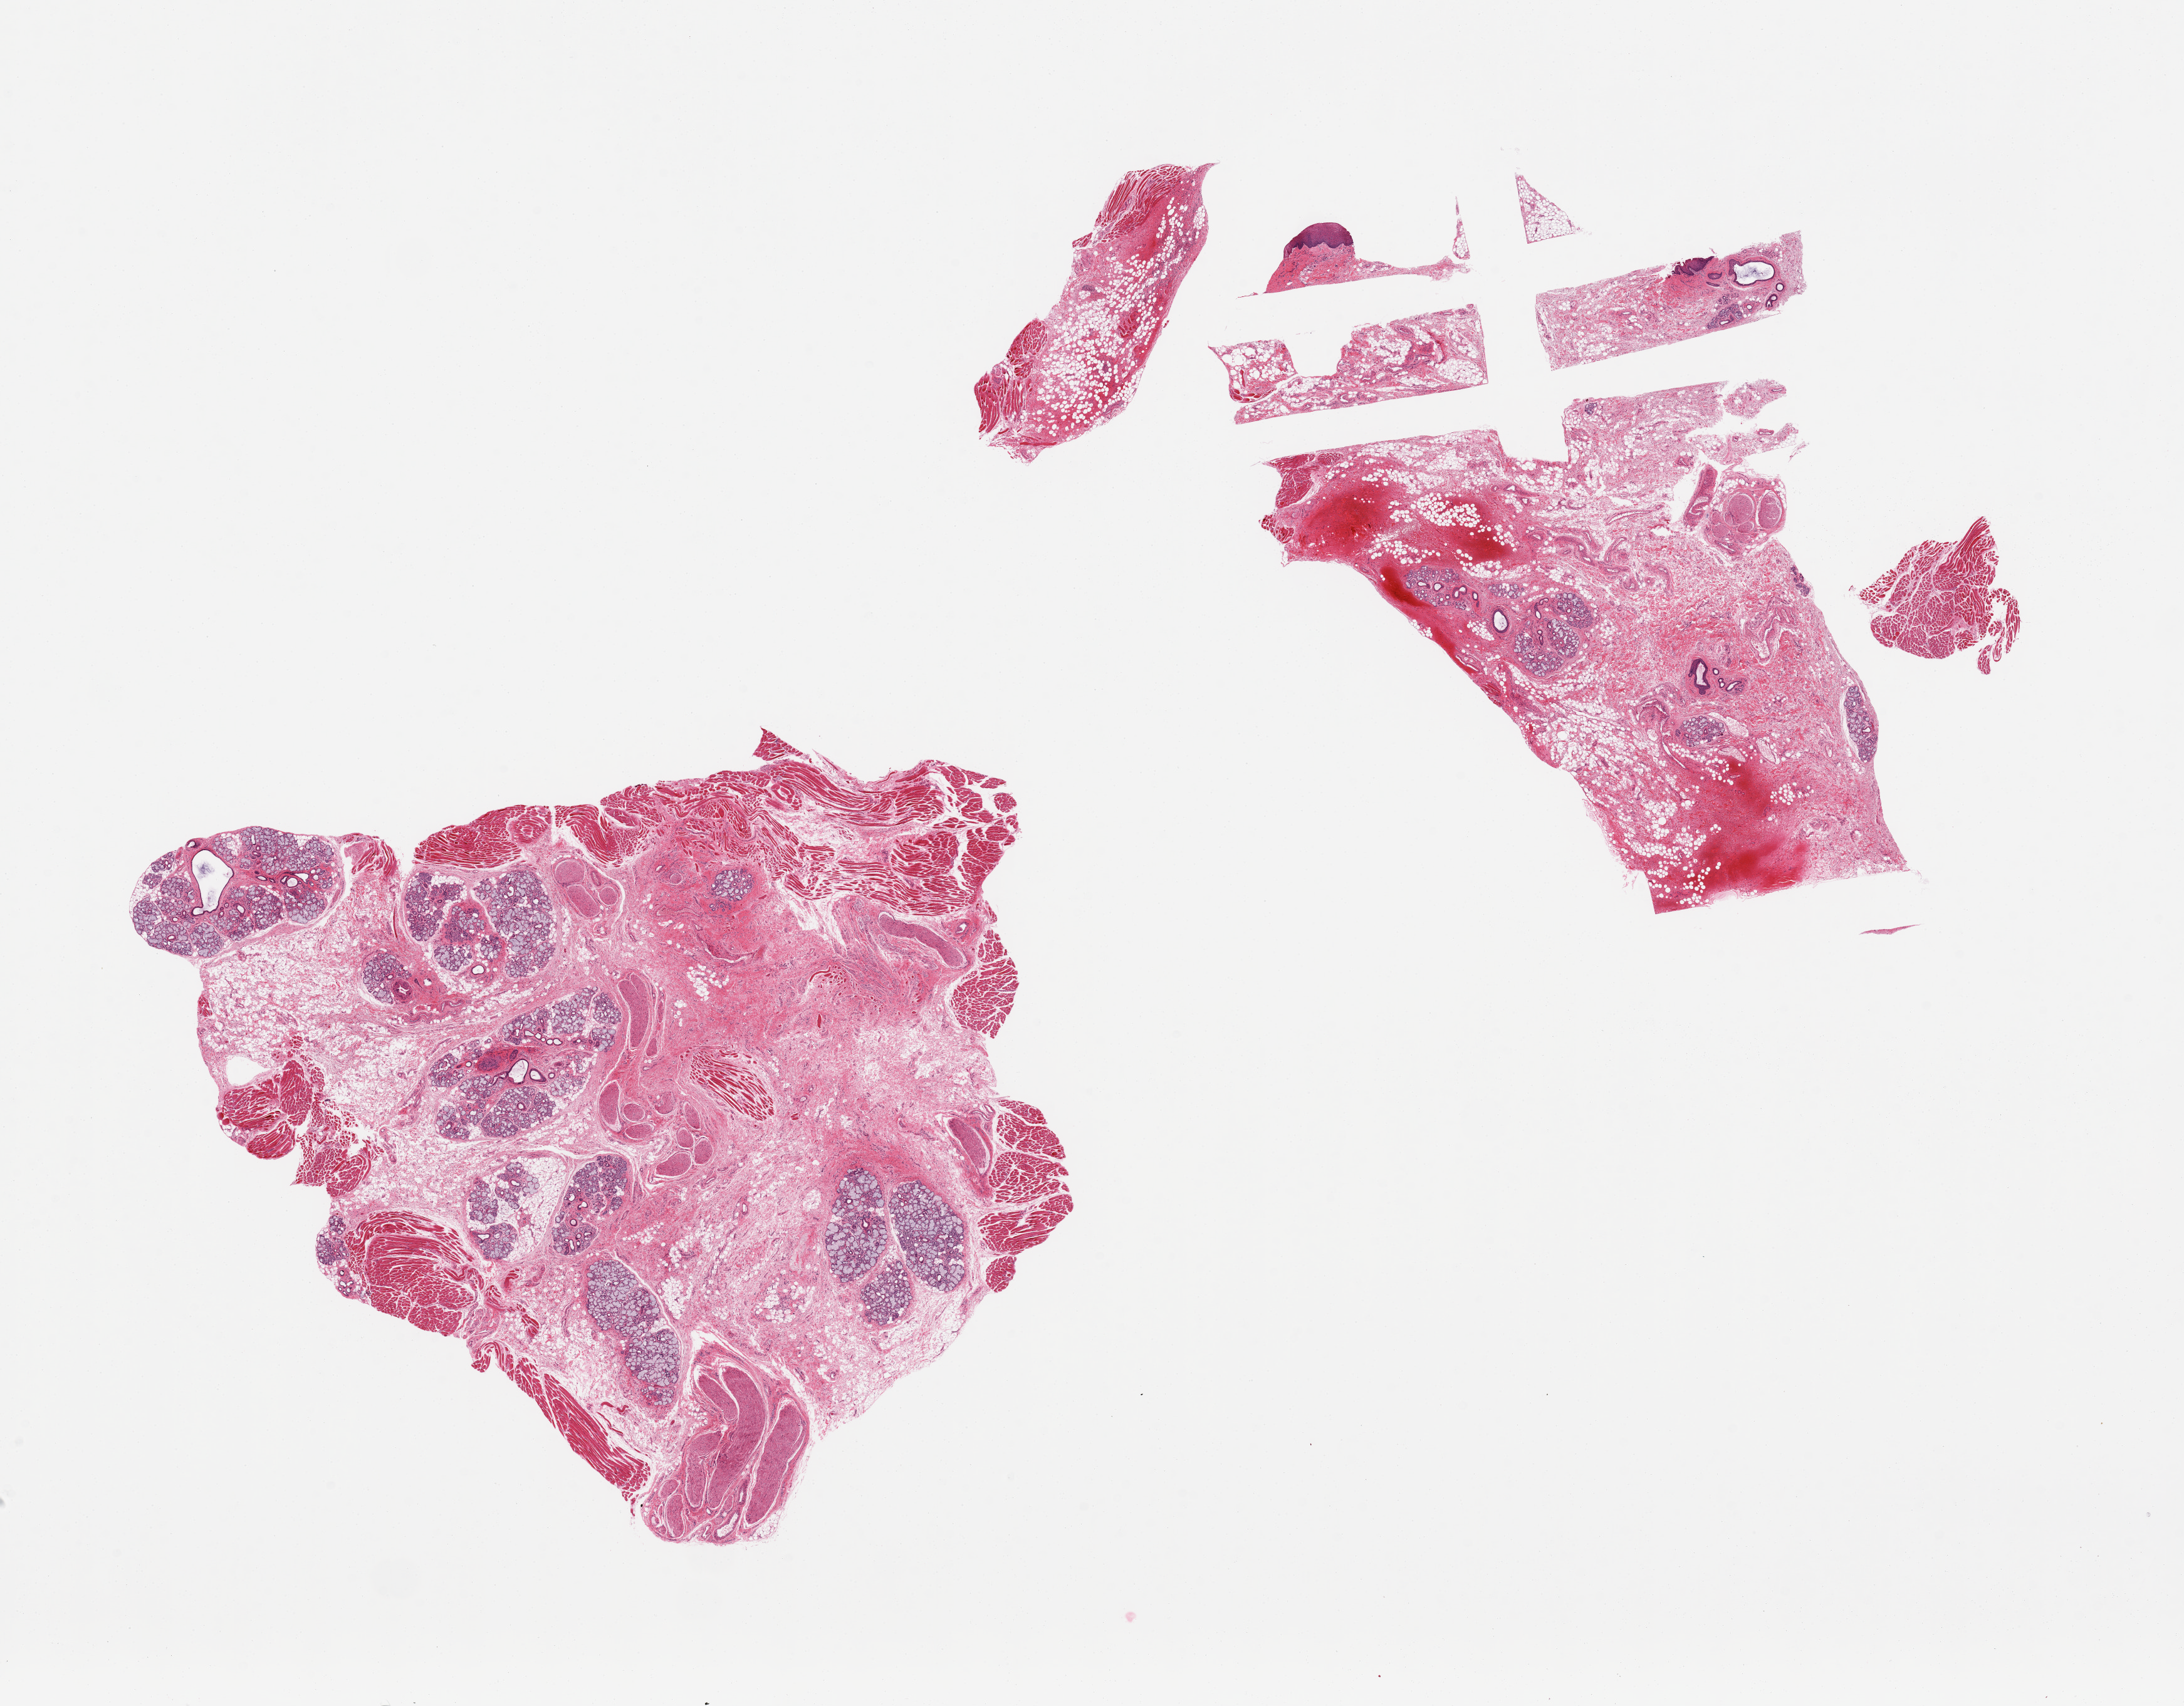
Digitized haematoxylin and eosin-stained section, brightfield, shown as a low-resolution overview of the whole scanned area (about 27.6 x 21.5 mm), PAXgene-fixed, paraffin-embedded tissue, section of minor salivary gland (target tissue), donor tissue sample. Donor sex: male.
• review note (as recorded): 2 pieces, salivary gland represents ~20% of the tissue, remainder is skeletal muscle, stroma, fat, nerve and small focus of lip/squamous epithelium